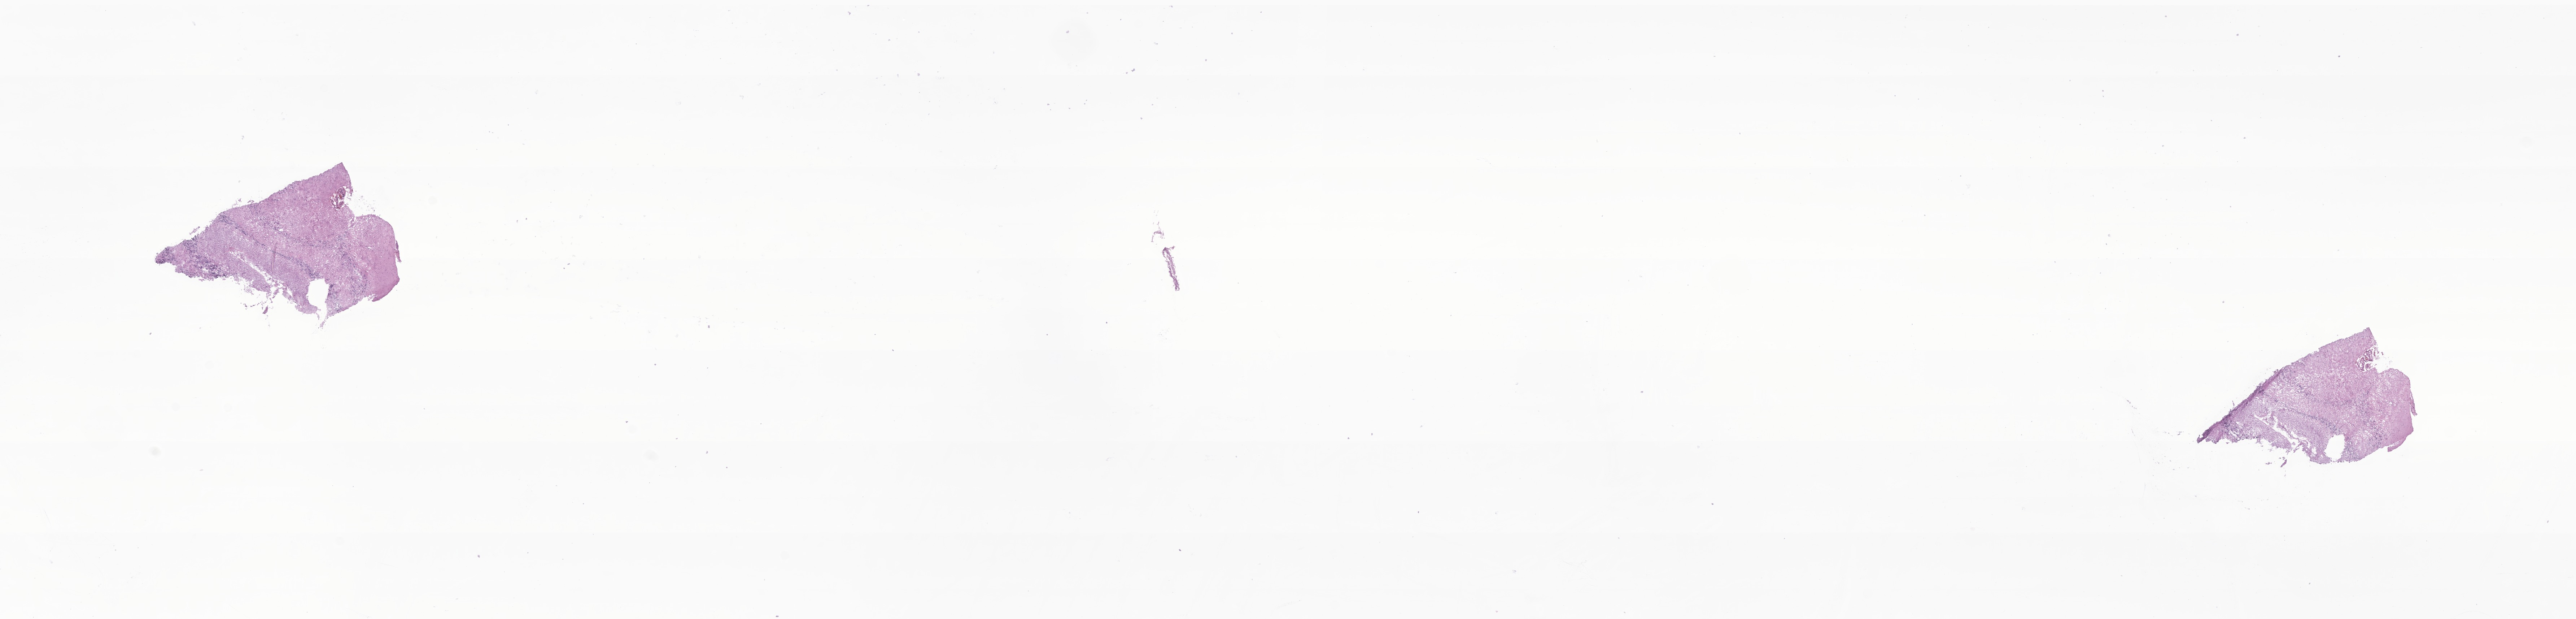
Whole-slide image, hematoxylin and eosin (H&E) stain of tumor tissue from the brain — a low-resolution overview of the entire scanned area, about 30.1 x 7.2 mm, cryosection (OCT / tissue freezing medium). Female patient, age 774 days (about 2.1 years).
Diagnosis: Pilocytic astrocytoma.